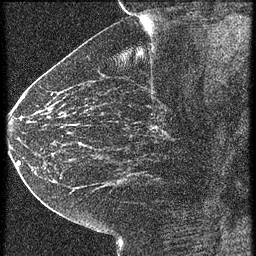
Breast MRI (dynamic contrast-enhanced), one sagittal slice. Position 31 of 60 along the scan axis. 4 images stored at this slice position (order not interpretable as contrast timing). 1.5 T. TE 4.2 ms, TR 21.3 ms. 1.5 mm slice thickness. 256 × 256 image matrix. Patient: female, 43 years. Case-level facts recorded for this patient, not image findings: setting: breast cancer imaged before/during neoadjuvant chemotherapy; receptor status: HER2-positive.
Structures marked on this image (semi-automatic segmentation, software-assisted and operator-edited):
- analysis volume of interest (the breast-tissue region the enhancement analysis was run in; not a lesion): box from (x=122, y=100) to (x=187, y=151) px
- tumour enhancement mask (voxels above the 90 % enhancement threshold inside the analysis volume of interest): (x=154, y=126)–(x=157, y=129)